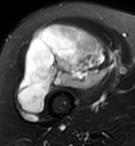
MRI of an extremity soft-tissue mass, one axial slice. Position 63 of 95 along the scan axis. T2-weighted fat-saturated. MR volume resampled by the dataset authors to the PET/CT grid (not the native acquisition matrix). 3.27 mm slice thickness. 135 × 146 image matrix, field of view 132 × 143 mm. Female patient. Case-level facts recorded for this patient, not image findings: histological type: pleiomorphic undifferentiated sarcoma; grade: high; site of the primary tumour: right quadricep.
Outlined on this slice (expert contour drawn on MRI and transferred to this co-registered scan by the dataset authors):
- gross tumour volume including surrounding oedema: bounding box [x1, y1, x2, y2] px = [18, 24, 111, 114]
- gross tumour volume (mass): [18, 24, 111, 114]